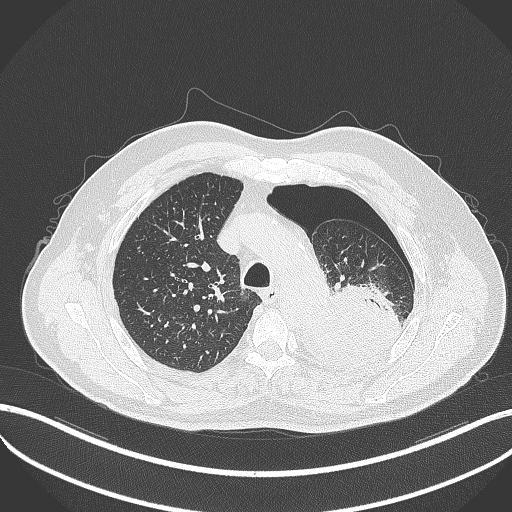
Chest CT, one axial slice; position 383 of 464 along the scan axis; 120 kVp; lung window (W 1500 / L -600 HU); 512 × 512 image matrix, field of view 400 × 400 mm. Male patient, age 76 years. From the clinical record (not read from this slice): clinical TNM (as recorded): T3 N0 M1b.
Structures marked on this image (bounding box drawn by a radiologist):
- lung tumour (recorded histology: adenocarcinoma): box from (x=292, y=281) to (x=405, y=370) px